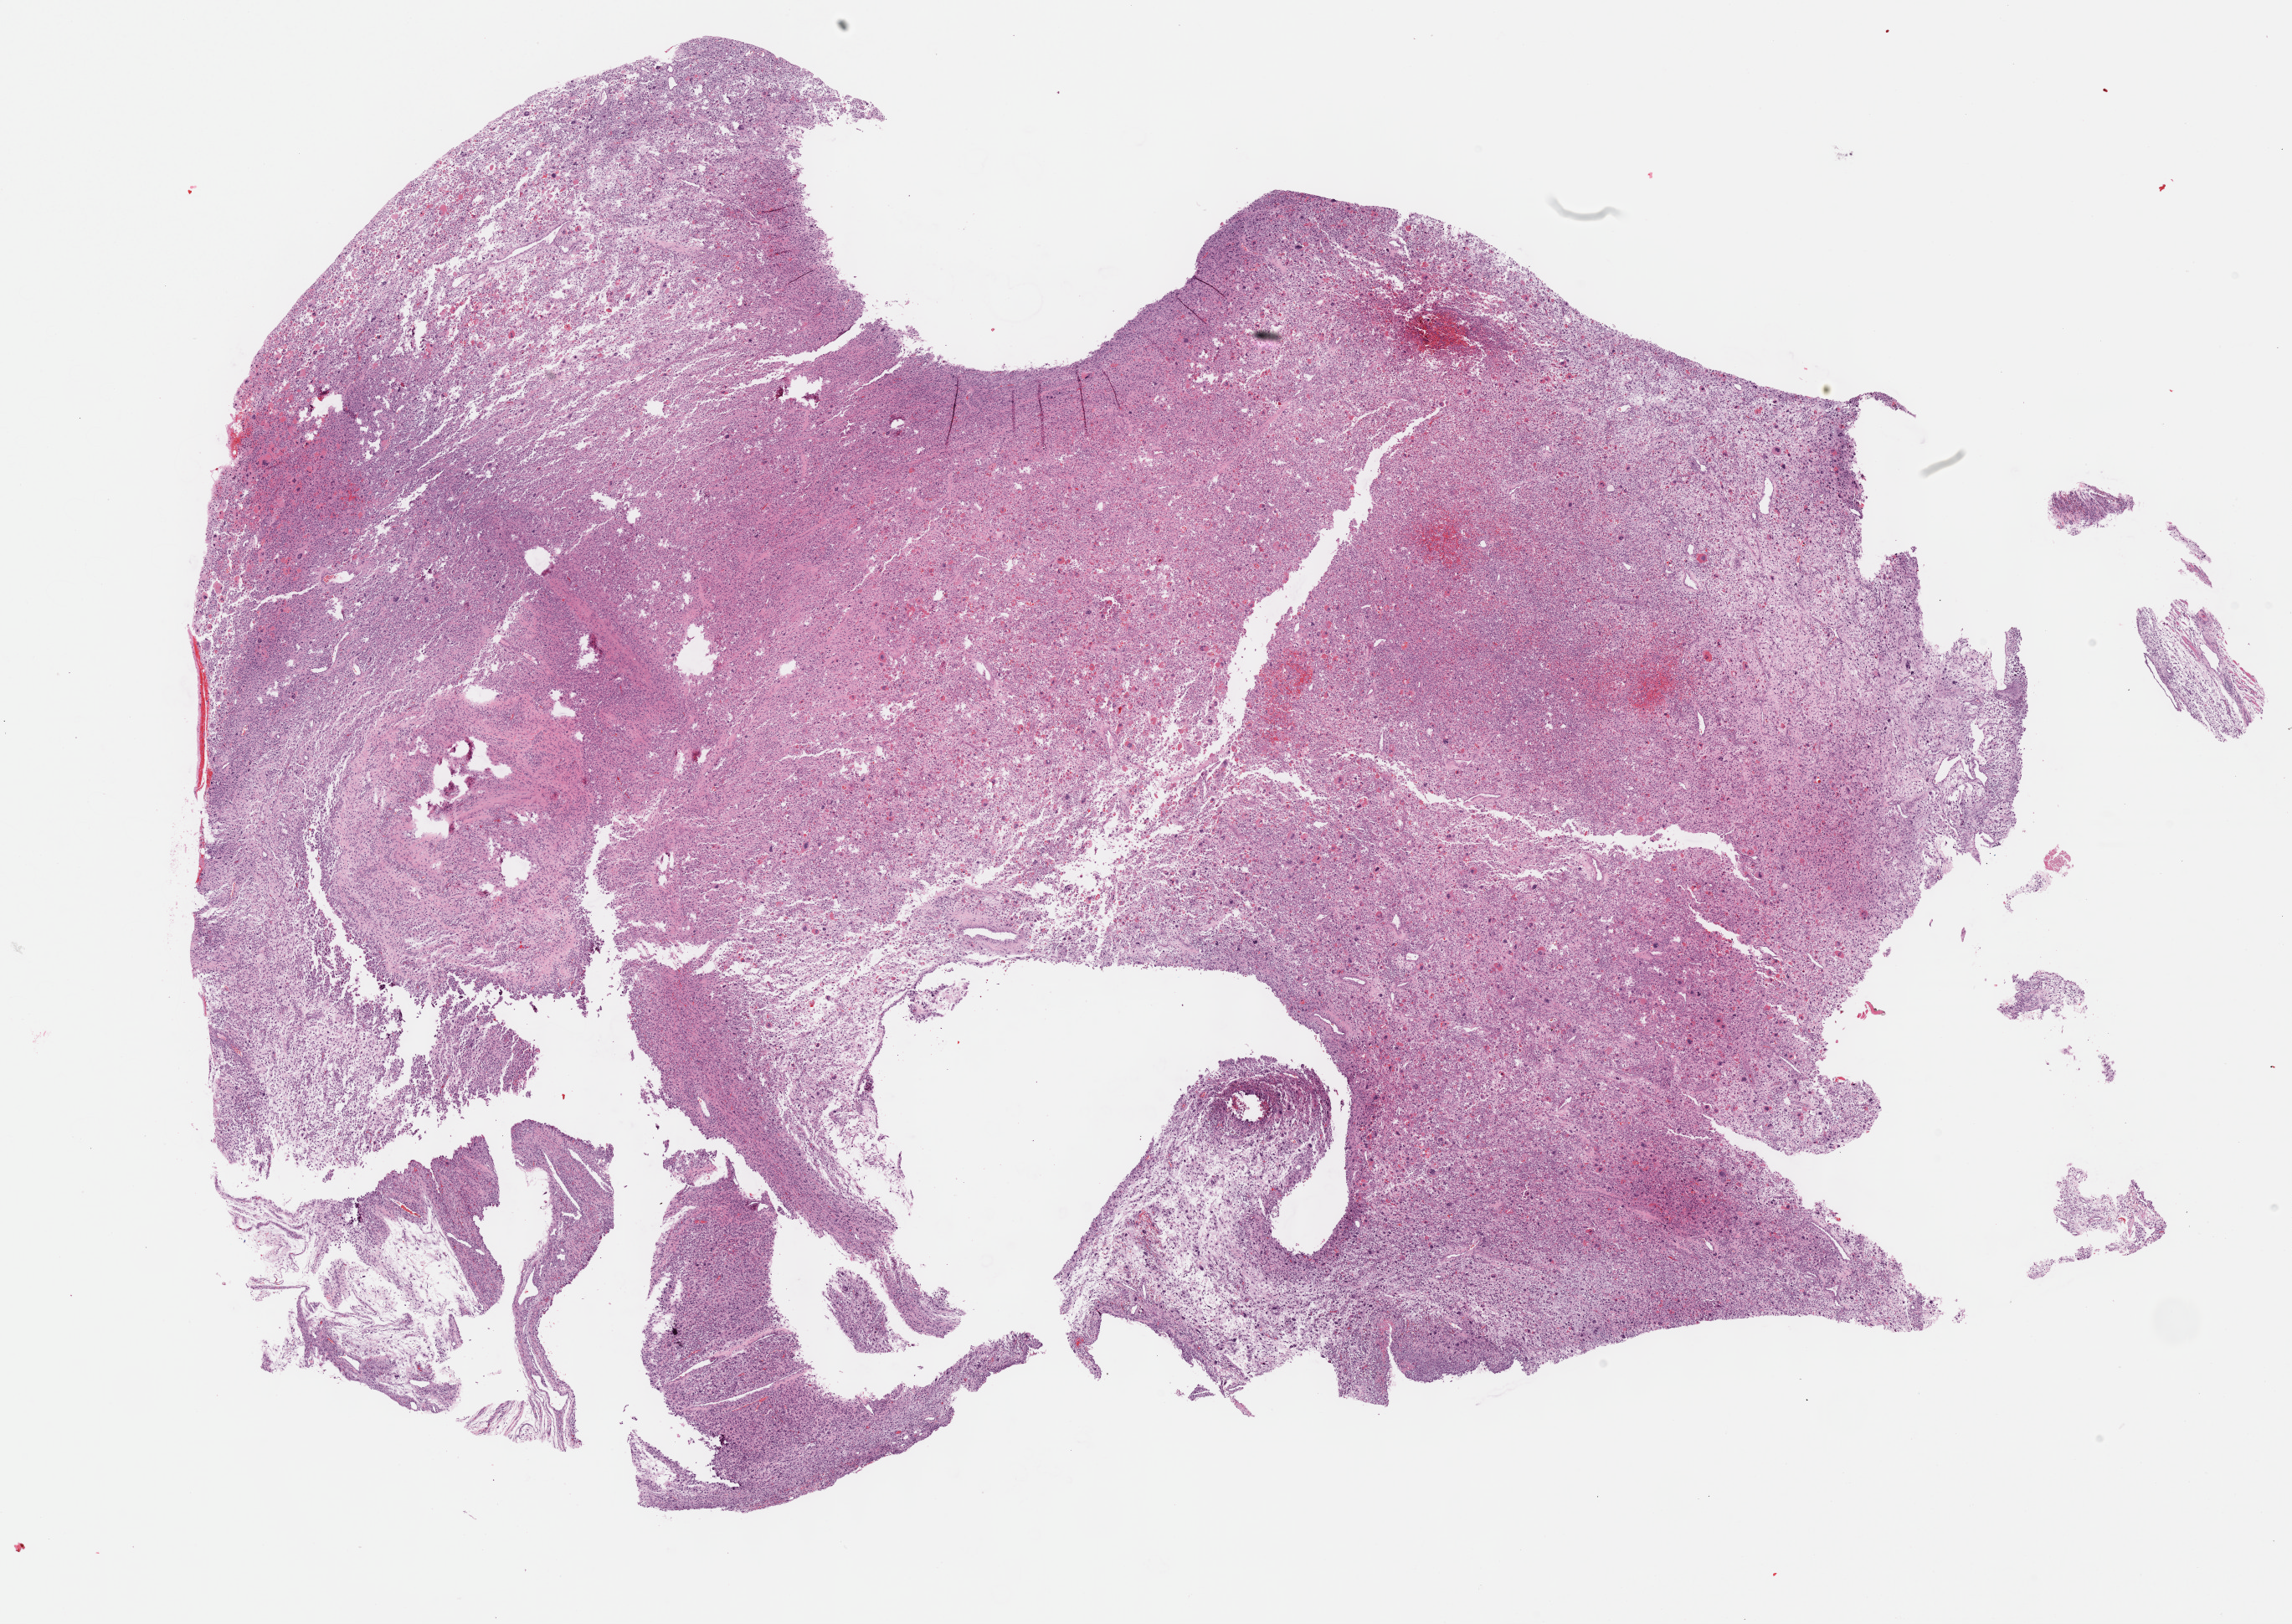
H&E-stained whole-slide image, whole scanned area (about 22.1 x 15.7 mm, slide scanned at 40x) shown as a low-resolution overview; formalin-fixed paraffin-embedded (FFPE) diagnostic section; connective, subcutaneous and other soft tissues, primary tumour sample. Female, age 54 years at initial diagnosis.
Diagnosis: Fibromyxosarcoma (connective, subcutaneous and other soft tissues of lower limb and hip).